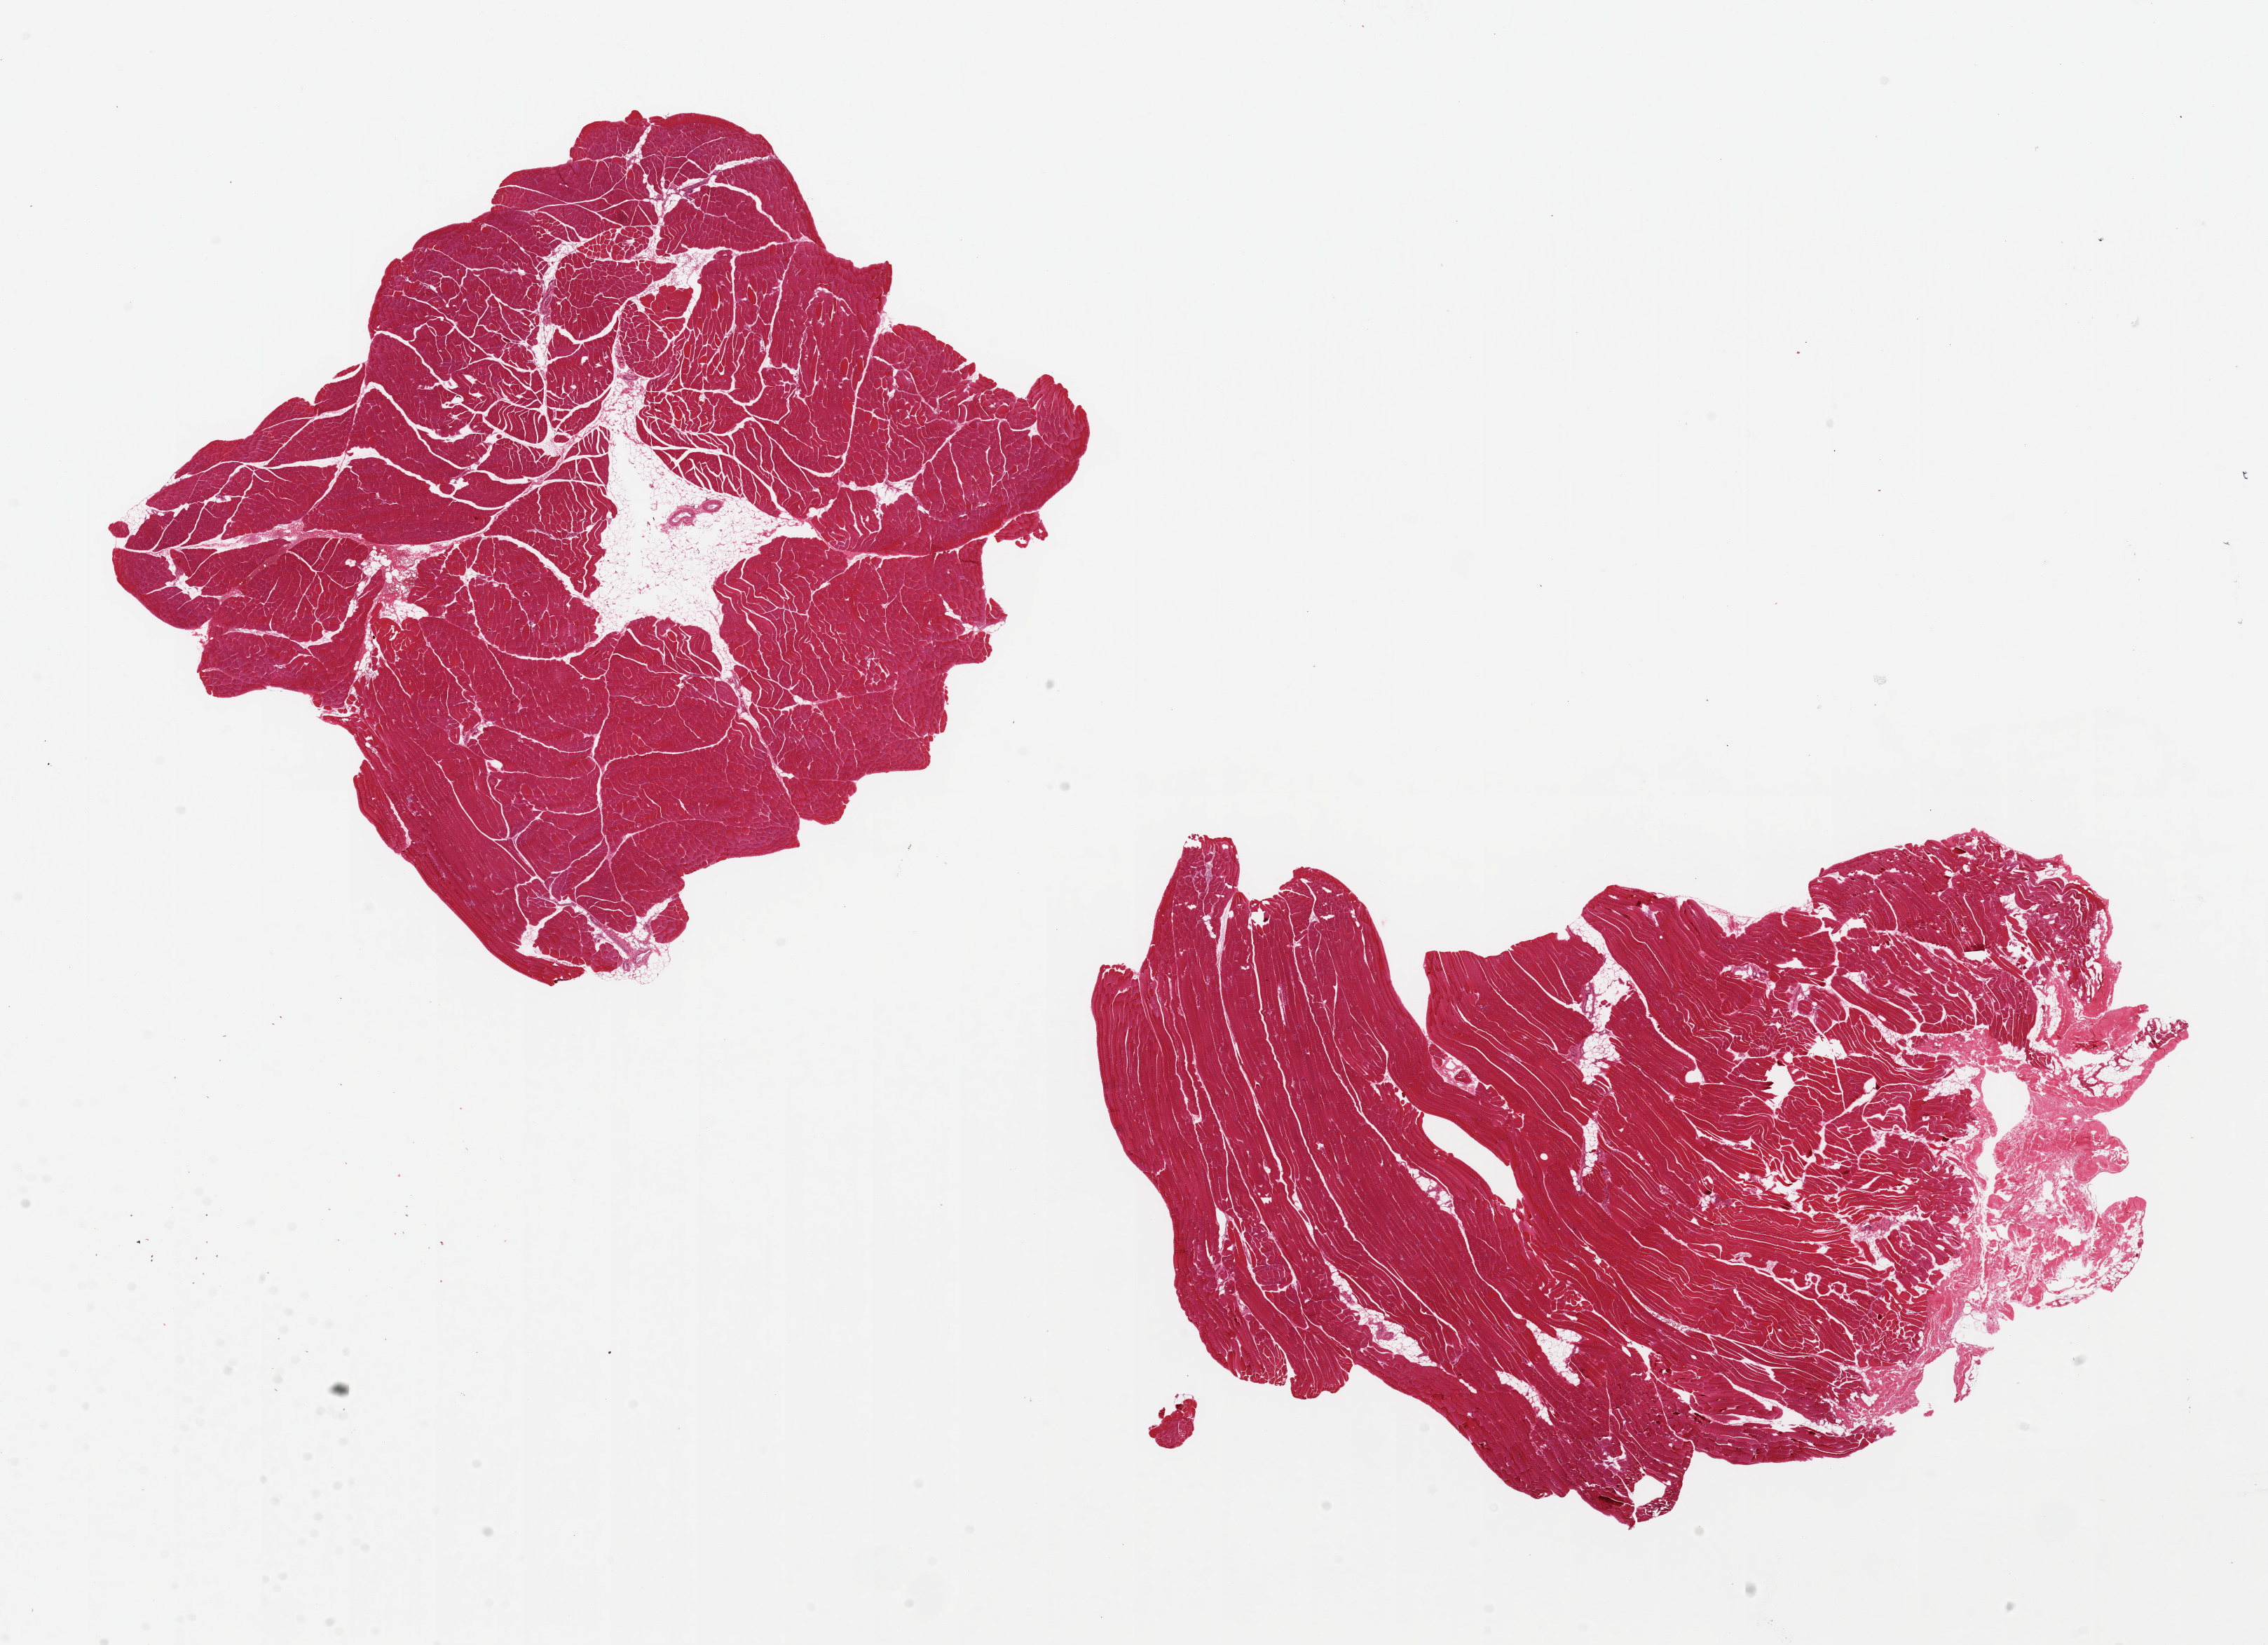
Digitized hematoxylin and eosin (H&E)-stained section, brightfield — shown as a low-resolution overview of the whole scanned area (about 25.6 x 18.6 mm, from a 20x scan). PAXgene-fixed paraffin-embedded (PFPE) section. Section of skeletal muscle (target tissue). Tissue donor sample. Donor: male.
* reviewer comment on this tissue sample: 2 pieces, 8x8 & 12x9mm; ~10% internal and external adipose and fibrous tissue